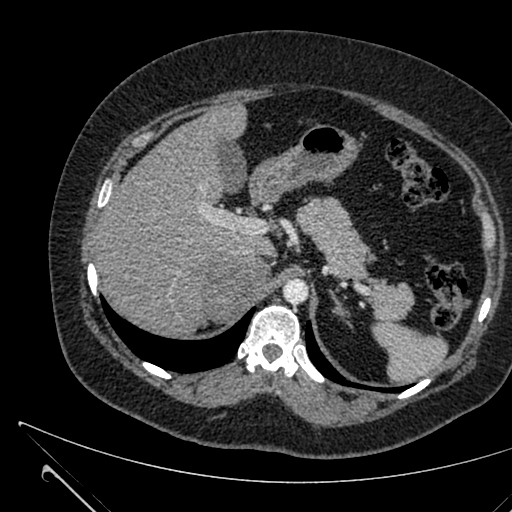
Contrast-enhanced abdominal CT, one axial slice; slice 465 of 731 in the series (ordered by position); 120 kVp; intravenous contrast given; soft-tissue window (W 400 / L 40 HU); 1 mm slice thickness; 512 × 512 image matrix, field of view 376 × 376 mm. Female patient, age 36 years. Case-level facts recorded for this patient, not image findings: diagnosis: adrenocortical carcinoma; tumour side: right adrenal; tumour size at pathology: 10 cm; Ki-67 index: 20 %; stage (as recorded): 4.
Structures marked on this image (semi-automatic segmentation, software-assisted and operator-edited):
- mass: bounding box [x1, y1, x2, y2] px = [200, 257, 269, 323]